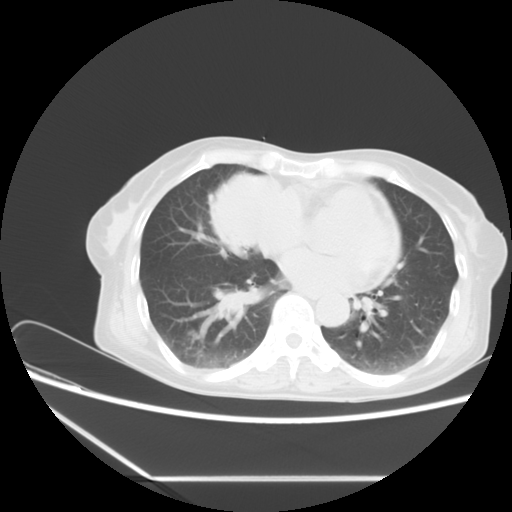
Chest CT, one axial slice. Position 1 of 16 along the scan axis. 120 kVp. Lung window (W 1500 / L -600 HU). 5 mm slice thickness. 512 × 512 image matrix. Patient: female, 63 years. Case-level facts recorded for this patient, not image findings: clinical TNM (as recorded): T2b N1 M0.
Annotated regions visible in this slice (rectangle marked by the reading radiologist):
- lung tumour (recorded histology: adenocarcinoma): bounding box [x1, y1, x2, y2] px = [199, 164, 283, 262]